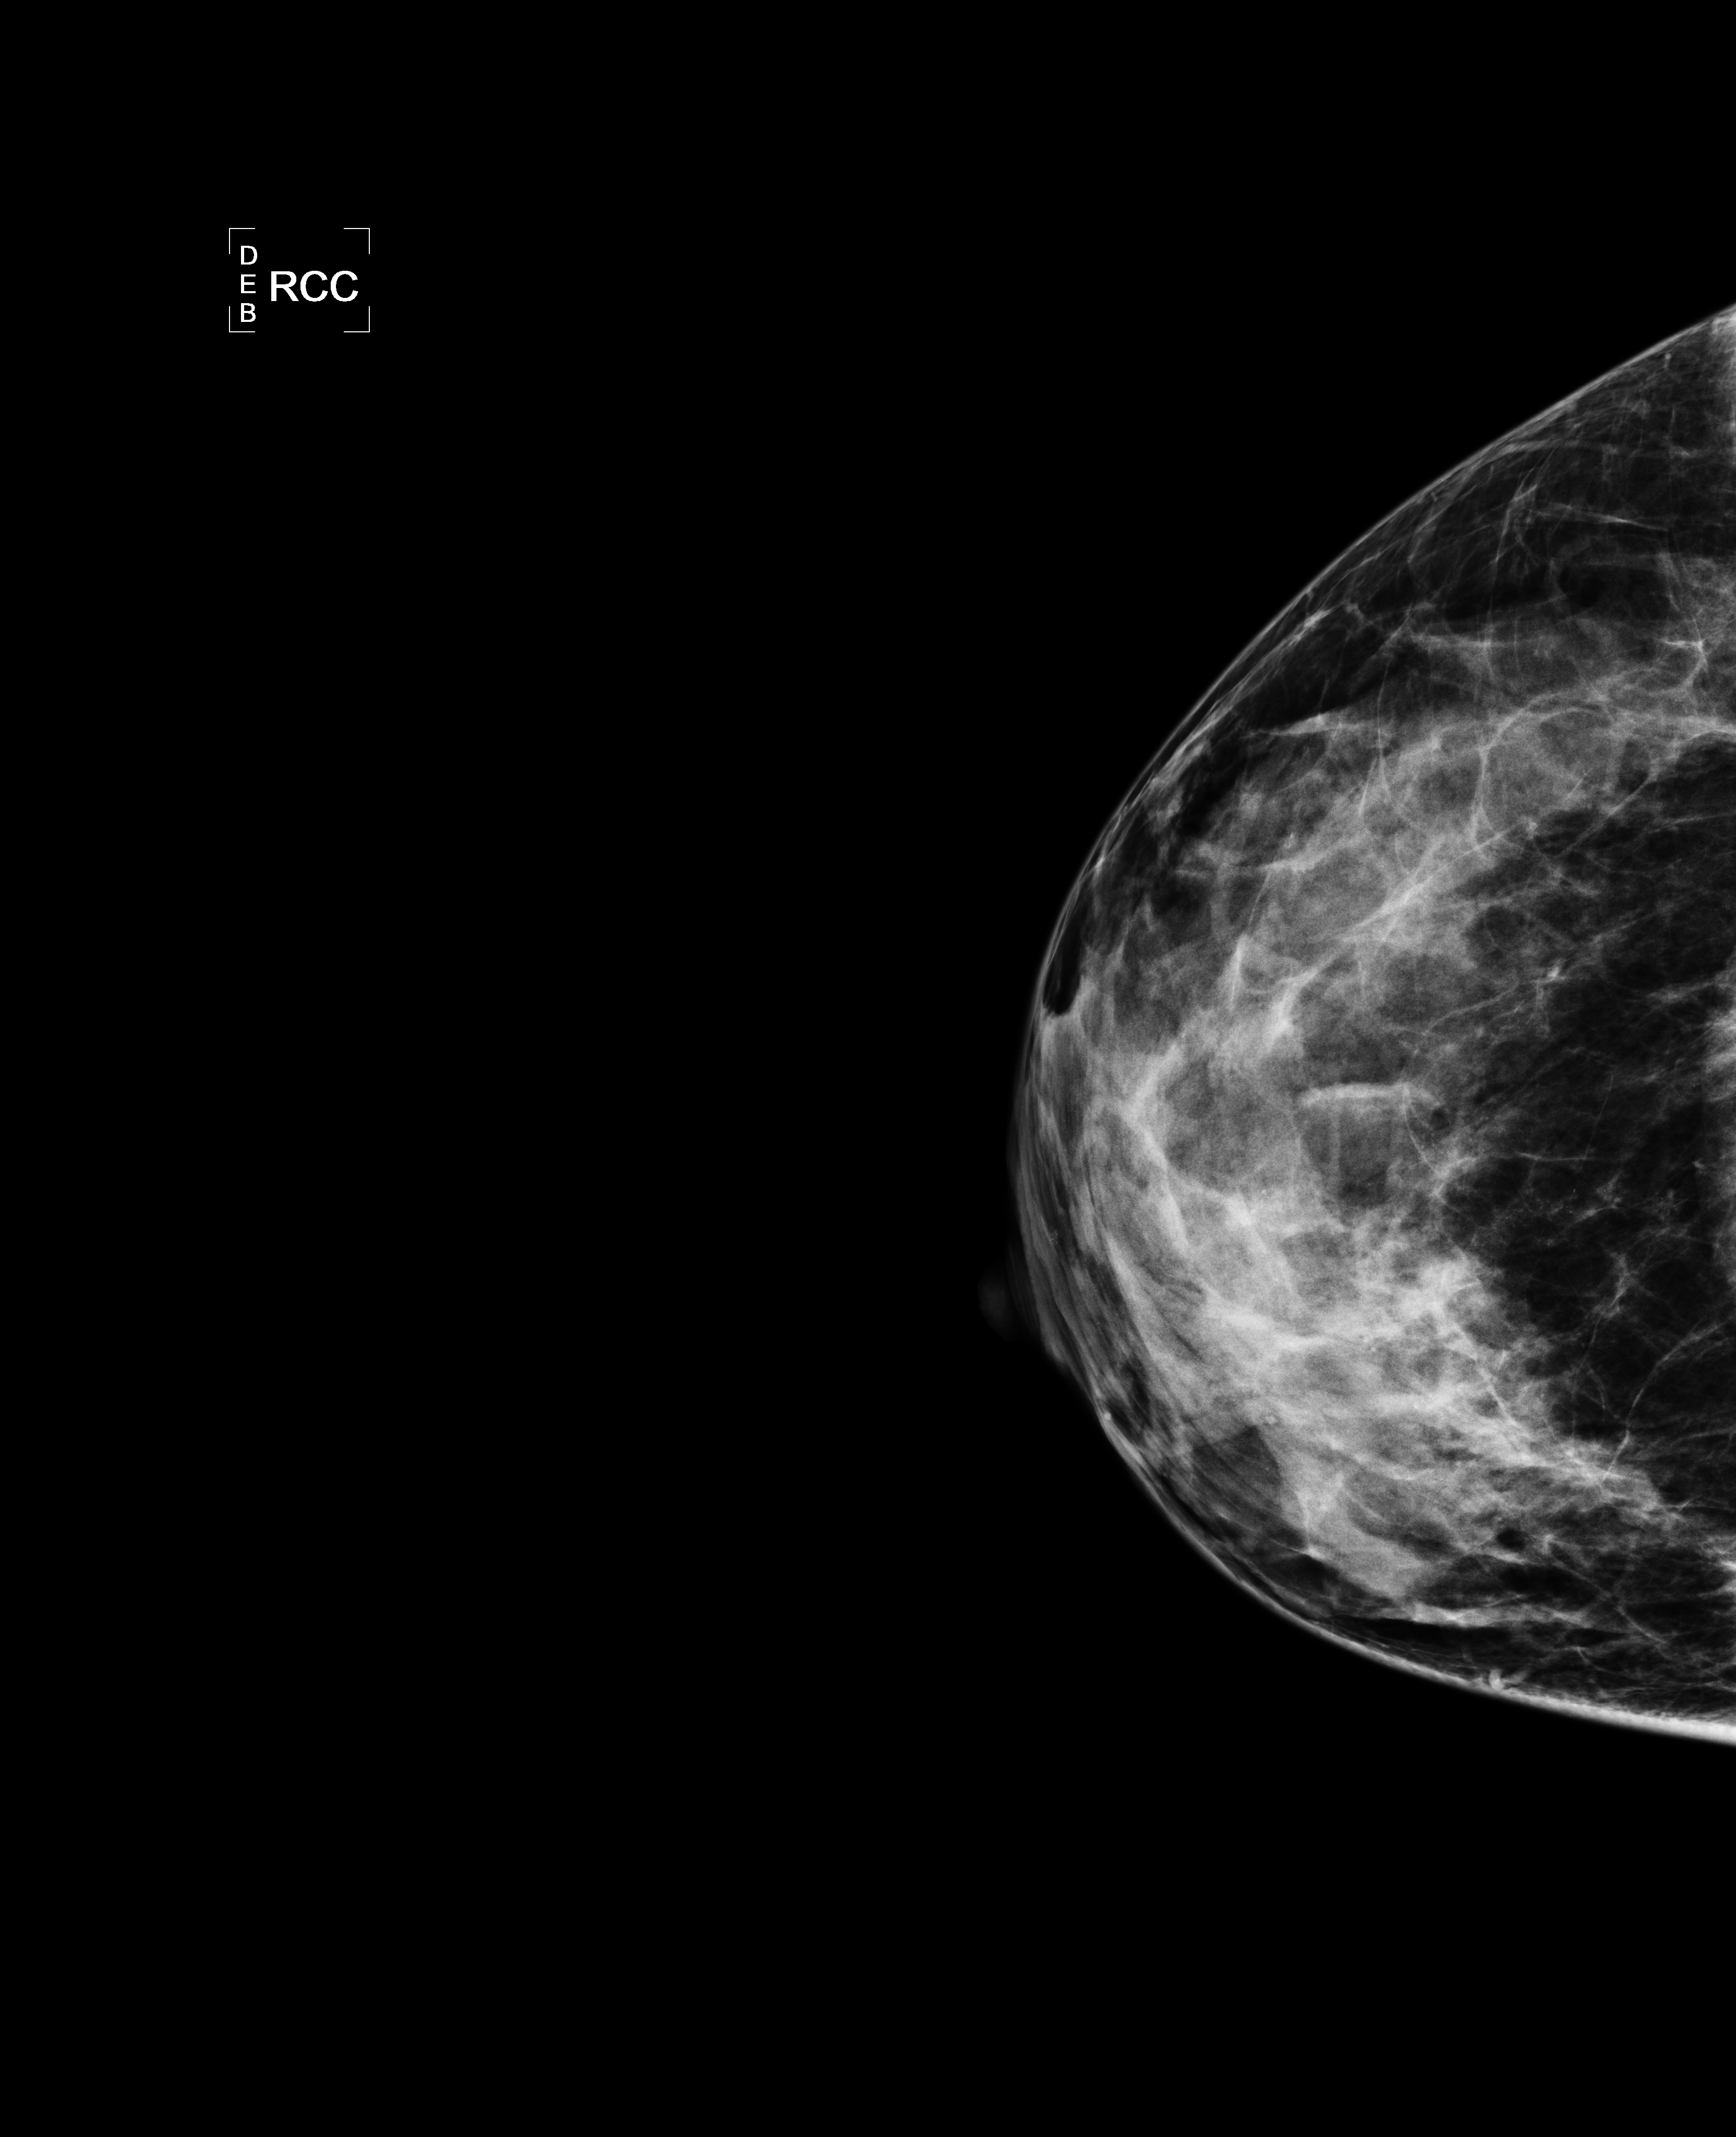
Mammogram, right breast, CC view.
Pathology recorded for this patient (not read from this image): pathology diagnosis: INVASIVE DUCTAL CARCINOMA, MODIFIED SCARFF-BLOOM-RICHARDSON GRADE-I/III. A LESS THAN 5% INTRADUCTAL CARCINOMA COMPONENT, NUCLEAR GRADE-II/III, IS ALSO PRESENT. (left breast); receptor status (as recorded): ER pos (strong), PR pos (strong), HER2 pos; Ki-67 (as recorded): intermed prolif; pathology report notes: mastectomy; INVASIVE DUCTAL CARCINOMA, MODIFIED SCARFF-BLOOM-RICHARDSON GRADE-I/III. A LESS THAN 5% INTRADUCTAL CARCINOMA COMPONENT, NUCLEAR GRADE-II/III, IS ALSO PRESENT; clinical background (as recorded): early 40s with left breast cancer. LMP unknown.